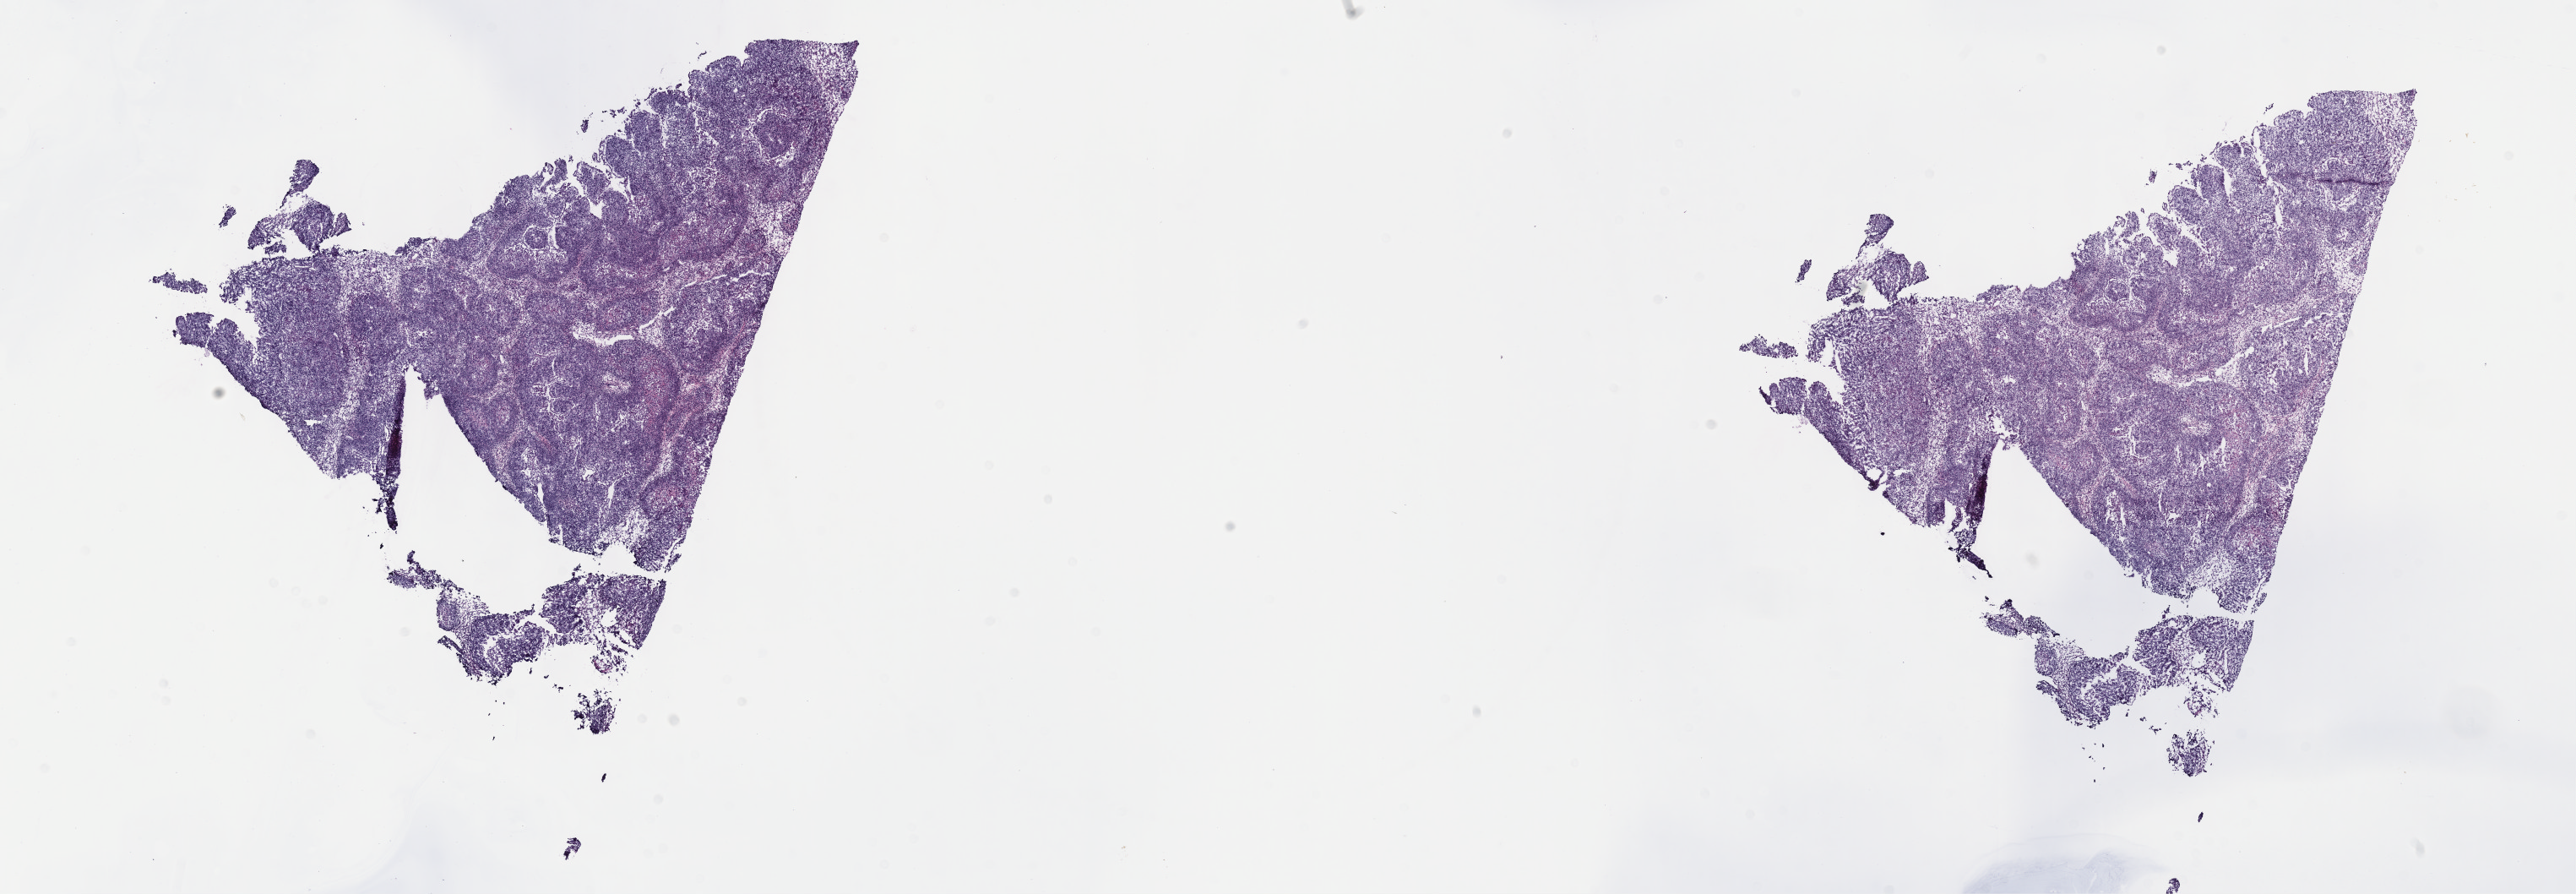
Whole-slide histology image, Hematoxylin and eosin (H&E) stained — whole scanned area (about 24.7 x 8.6 mm) shown as a low-resolution overview, frozen section from the top of the tissue portion, mesothelium, primary tumour sample. Patient: male, age at initial diagnosis 73 years. Composition of this section per pathologist review: tumour cells 100%, tumour nuclei 80%, normal cells 0%, stromal cells 0%, necrosis 0%. Infiltration values recorded for this section: lymphocyte infiltration 2%, monocyte infiltration 0%, neutrophil infiltration 0%.
AJCC pathologic stage: III (7th edition). Histologic diagnosis: Mesothelioma, biphasic, malignant (pleura, NOS).